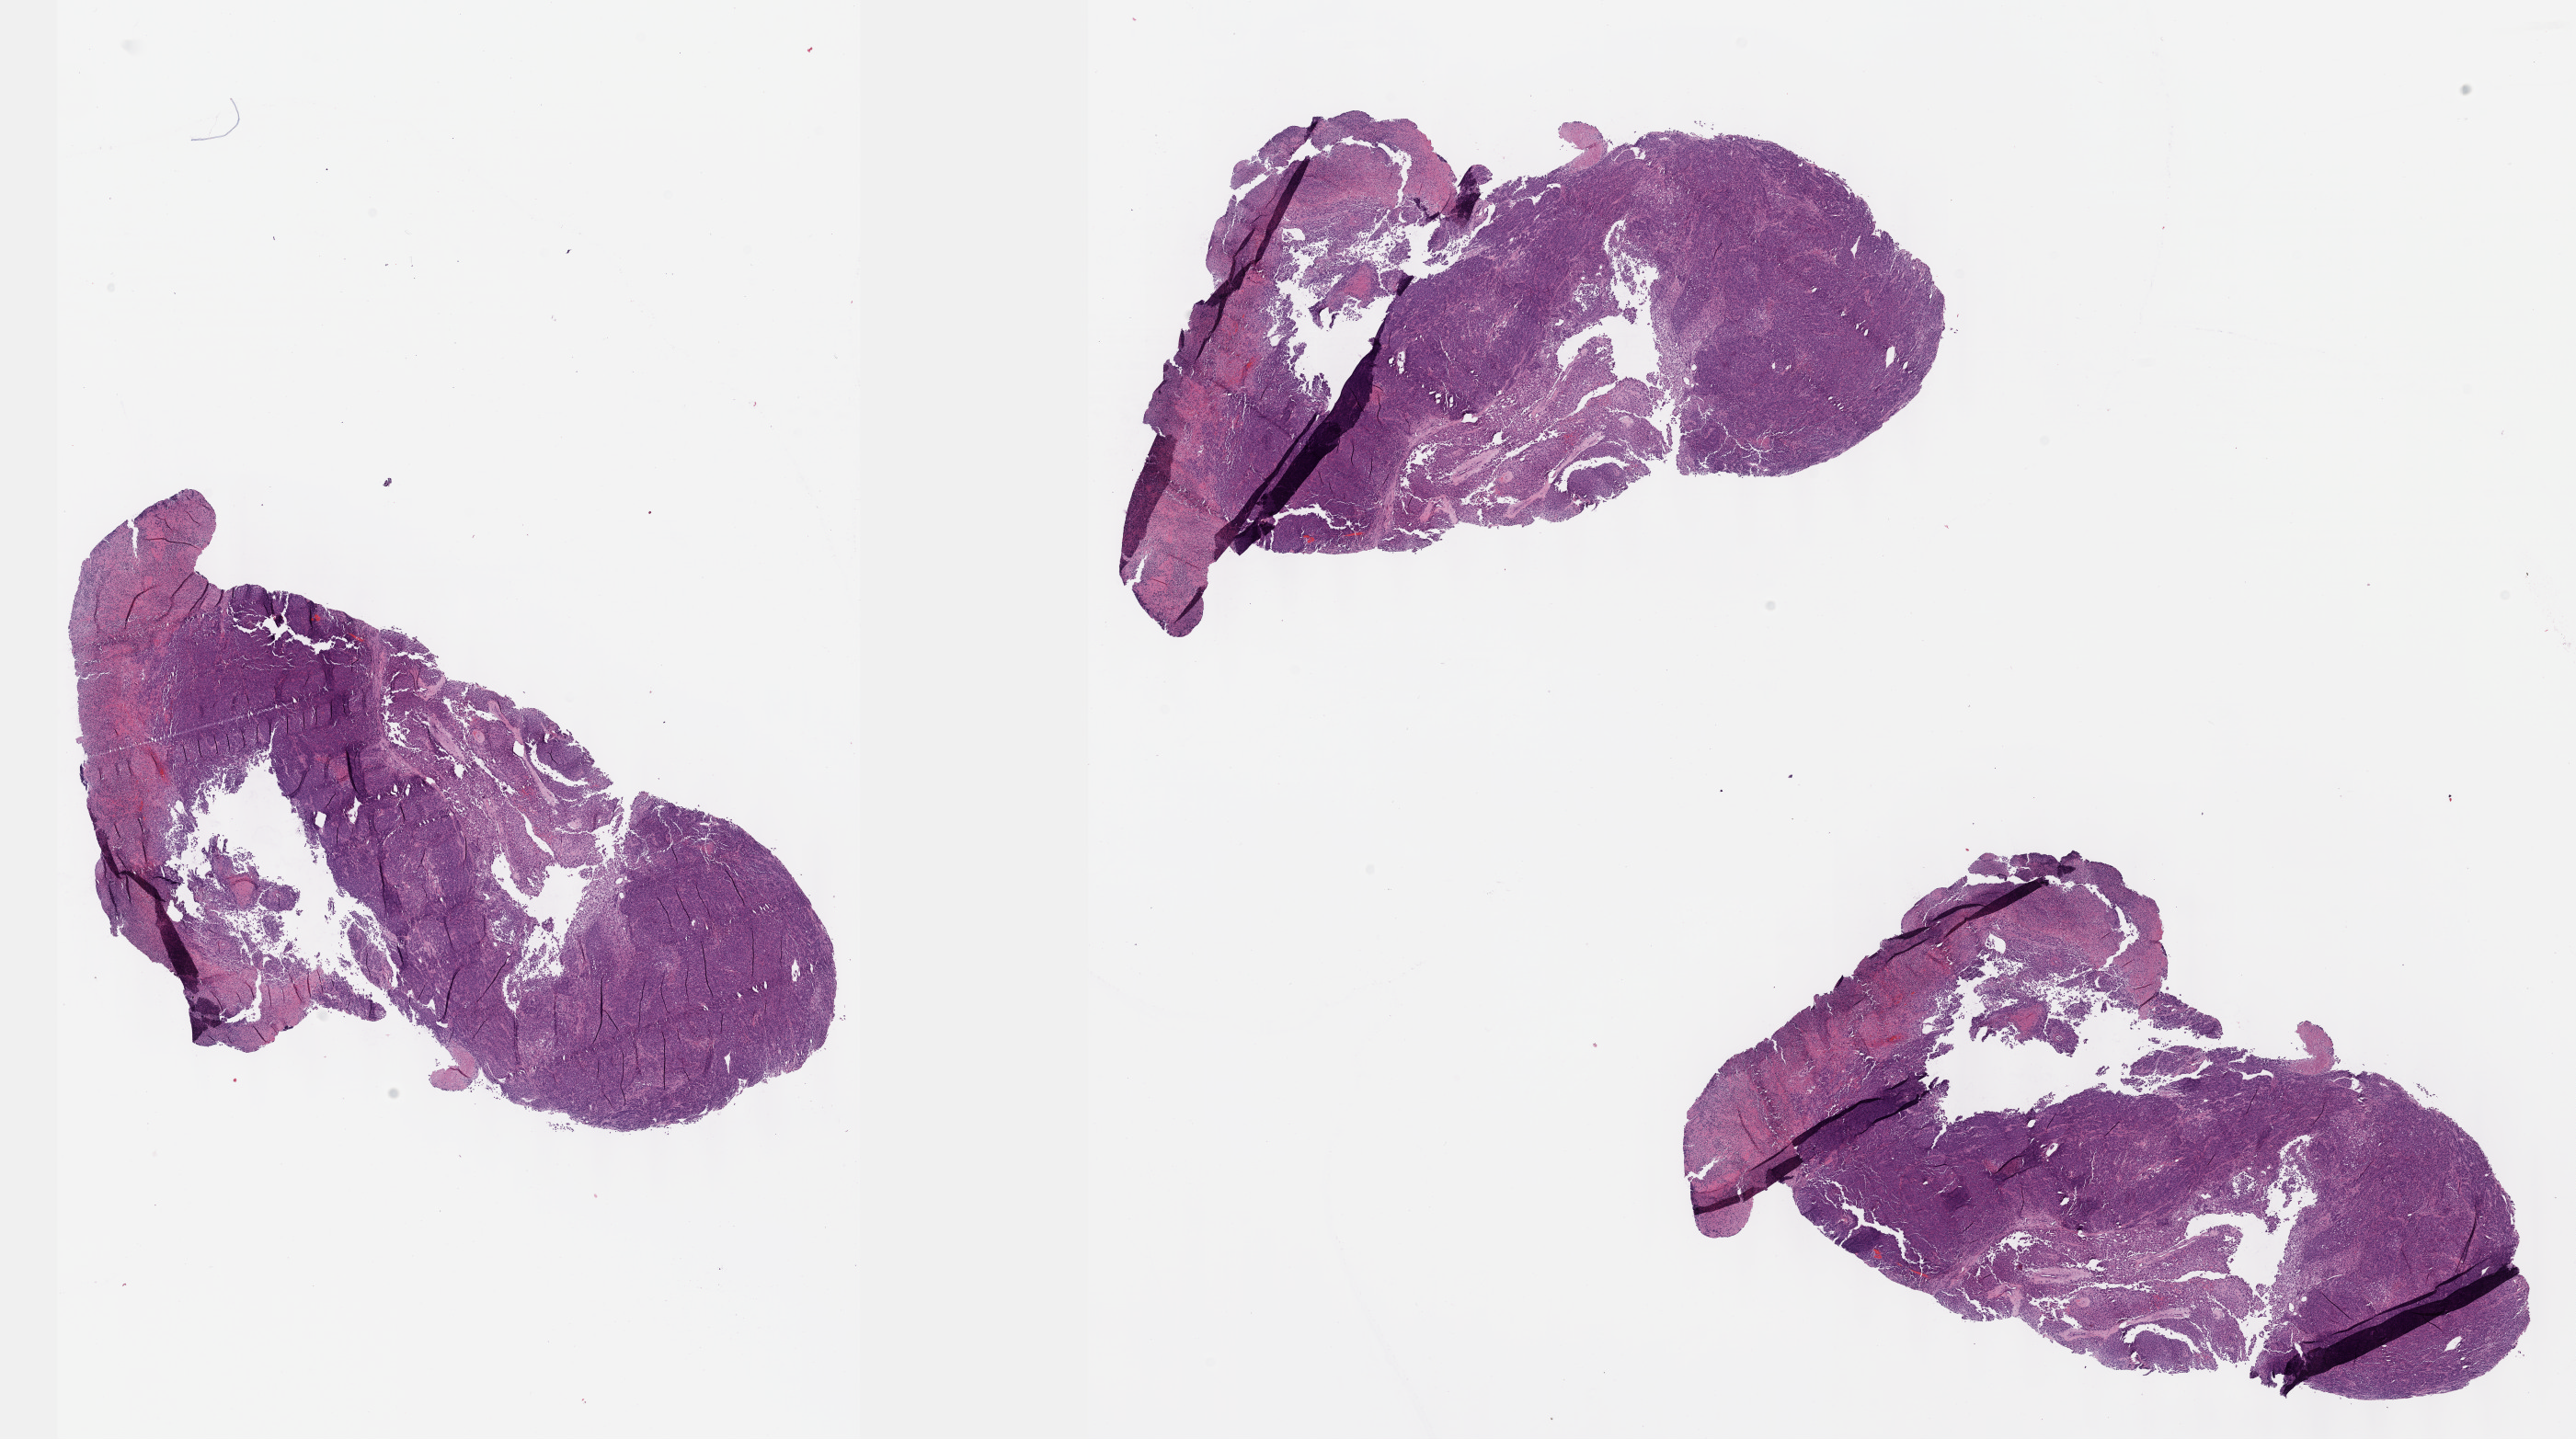
Hematoxylin and eosin (H&E) stained whole-slide image, a low-resolution overview of the entire scanned area, about 22.6 x 12.6 mm (from a 40x scan); FFPE section; primary tumour sample from the skin. Patient: male, age at initial diagnosis 39 years.
Diagnosis: Nodular melanoma. AJCC pathologic stage: IIC (7th edition). TNM: T4b NX M0.